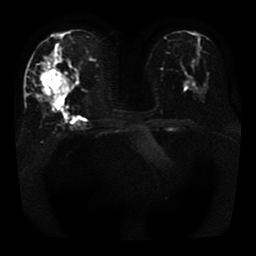
Breast MRI, one axial slice; position 18 of 41 along the scan axis; diffusion-weighted series; image 2 of 4 stored at this slice position (different b-values; order by instance number); 1.5 T; 5 mm slice thickness; 256 × 256 image matrix, field of view 330 × 330 mm. Female patient.
Annotated regions visible in this slice (manually delineated by an expert):
- tumour on diffusion-weighted imaging: bounding box [x1, y1, x2, y2] px = [41, 65, 71, 99]